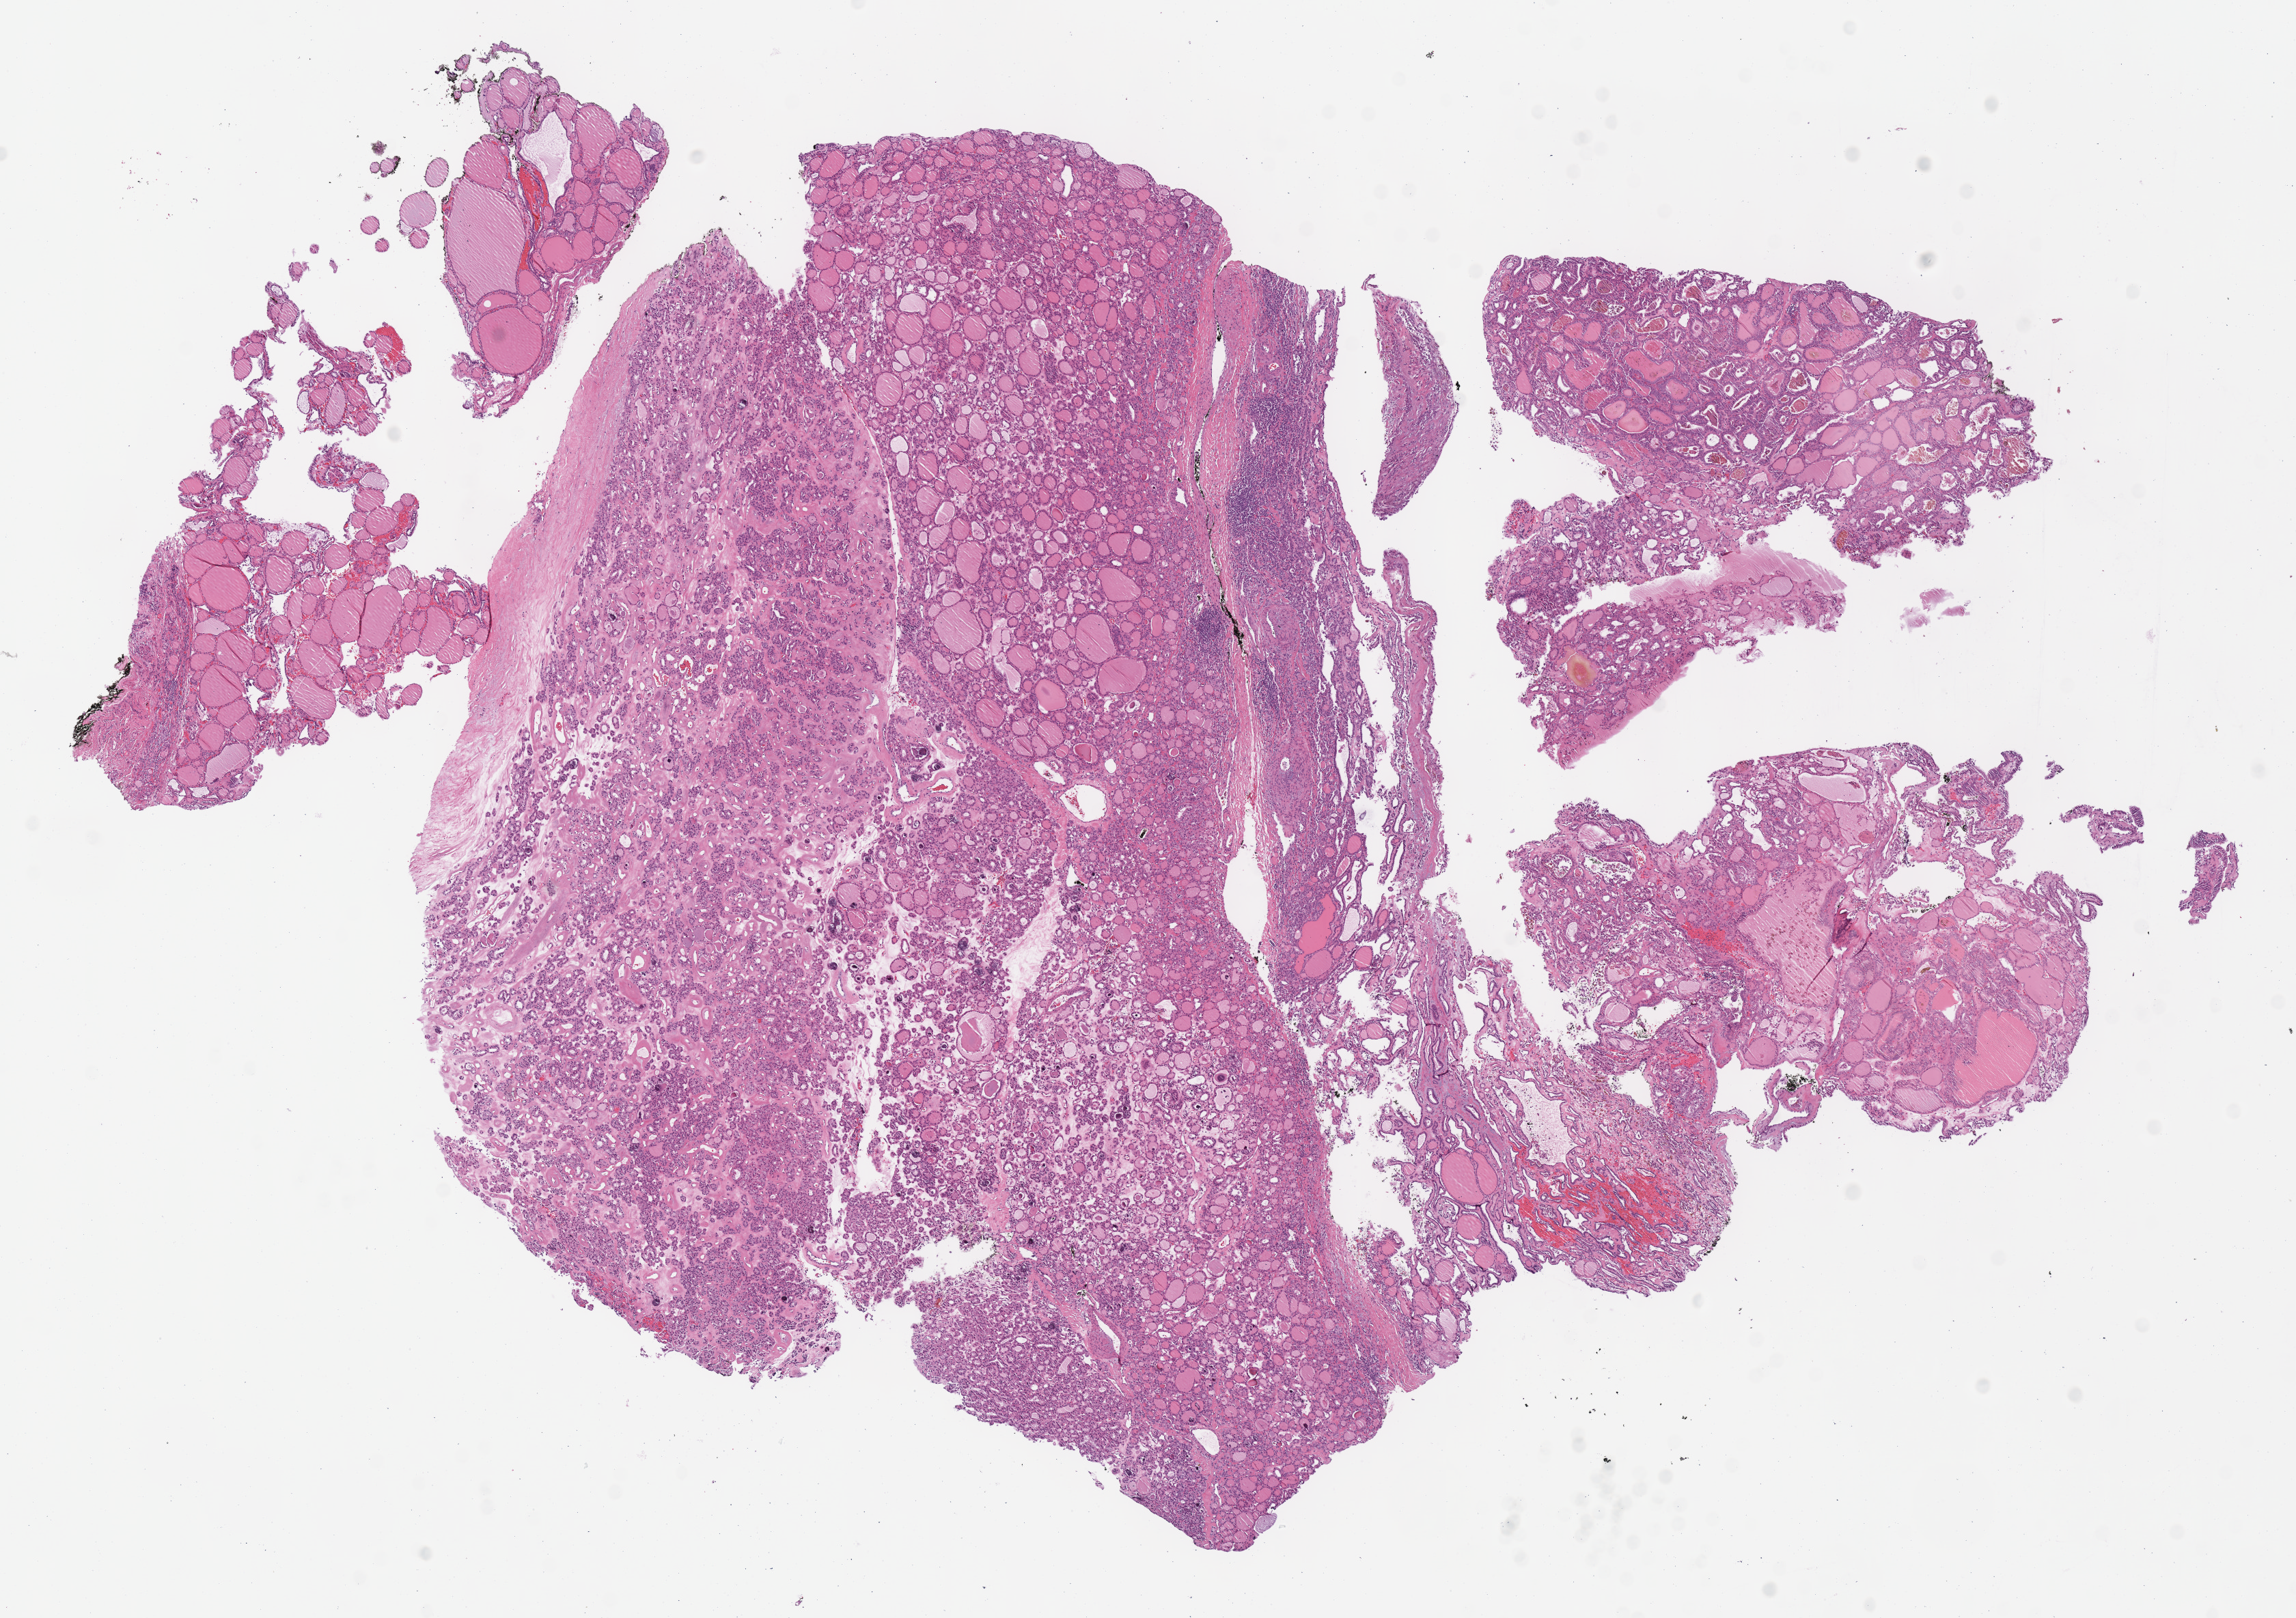
H&E whole-slide image, shown as a low-resolution overview of the whole scanned area (about 13.2 x 9.3 mm); formalin-fixed paraffin-embedded (FFPE) diagnostic section; primary tumour sample from the thyroid. Female, age 64 years at initial diagnosis.
* pathologic diagnosis: Papillary carcinoma, follicular variant (thyroid gland)
* lymph nodes positive (case pathology): 0 of 14 examined
* AJCC pathologic stage: III